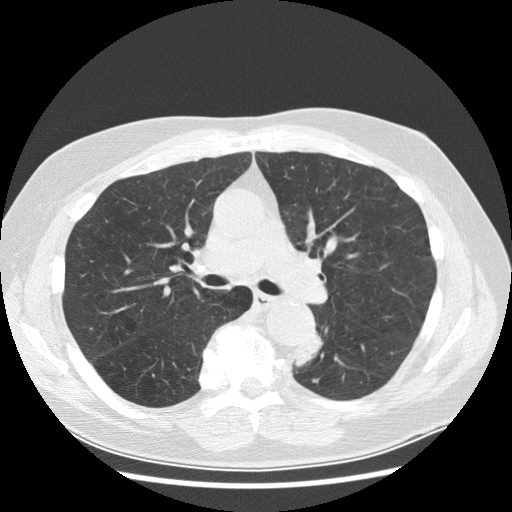
Low-dose screening chest CT, axial slice; first (baseline) screen; lung window (W 1500 / L -600 HU); 2.5 mm slice thickness; slice 108 of 282 in the series. Male participant, aged 70 years at enrolment.
• Expert-annotated lung lesion, bounding box (x1, y1, x2, y2) in pixels: (278, 327, 330, 384).
• Screening reader's record for this exam (one nodule recorded; not confirmed to be the boxed lesion): non-calcified nodule or mass ≥4 mm, left lower lobe, 27 × 16 mm, spiculated (stellate) margins, soft tissue attenuation, pre-existing on the prior screen: yes; interval growth: yes.
• Lung cancer was diagnosed 97 days after this screen: papillary adenocarcinoma, NOS, left lower lobe, moderately differentiated (G2), stage IB (AJCC 6th edition), 35 mm at pathology.